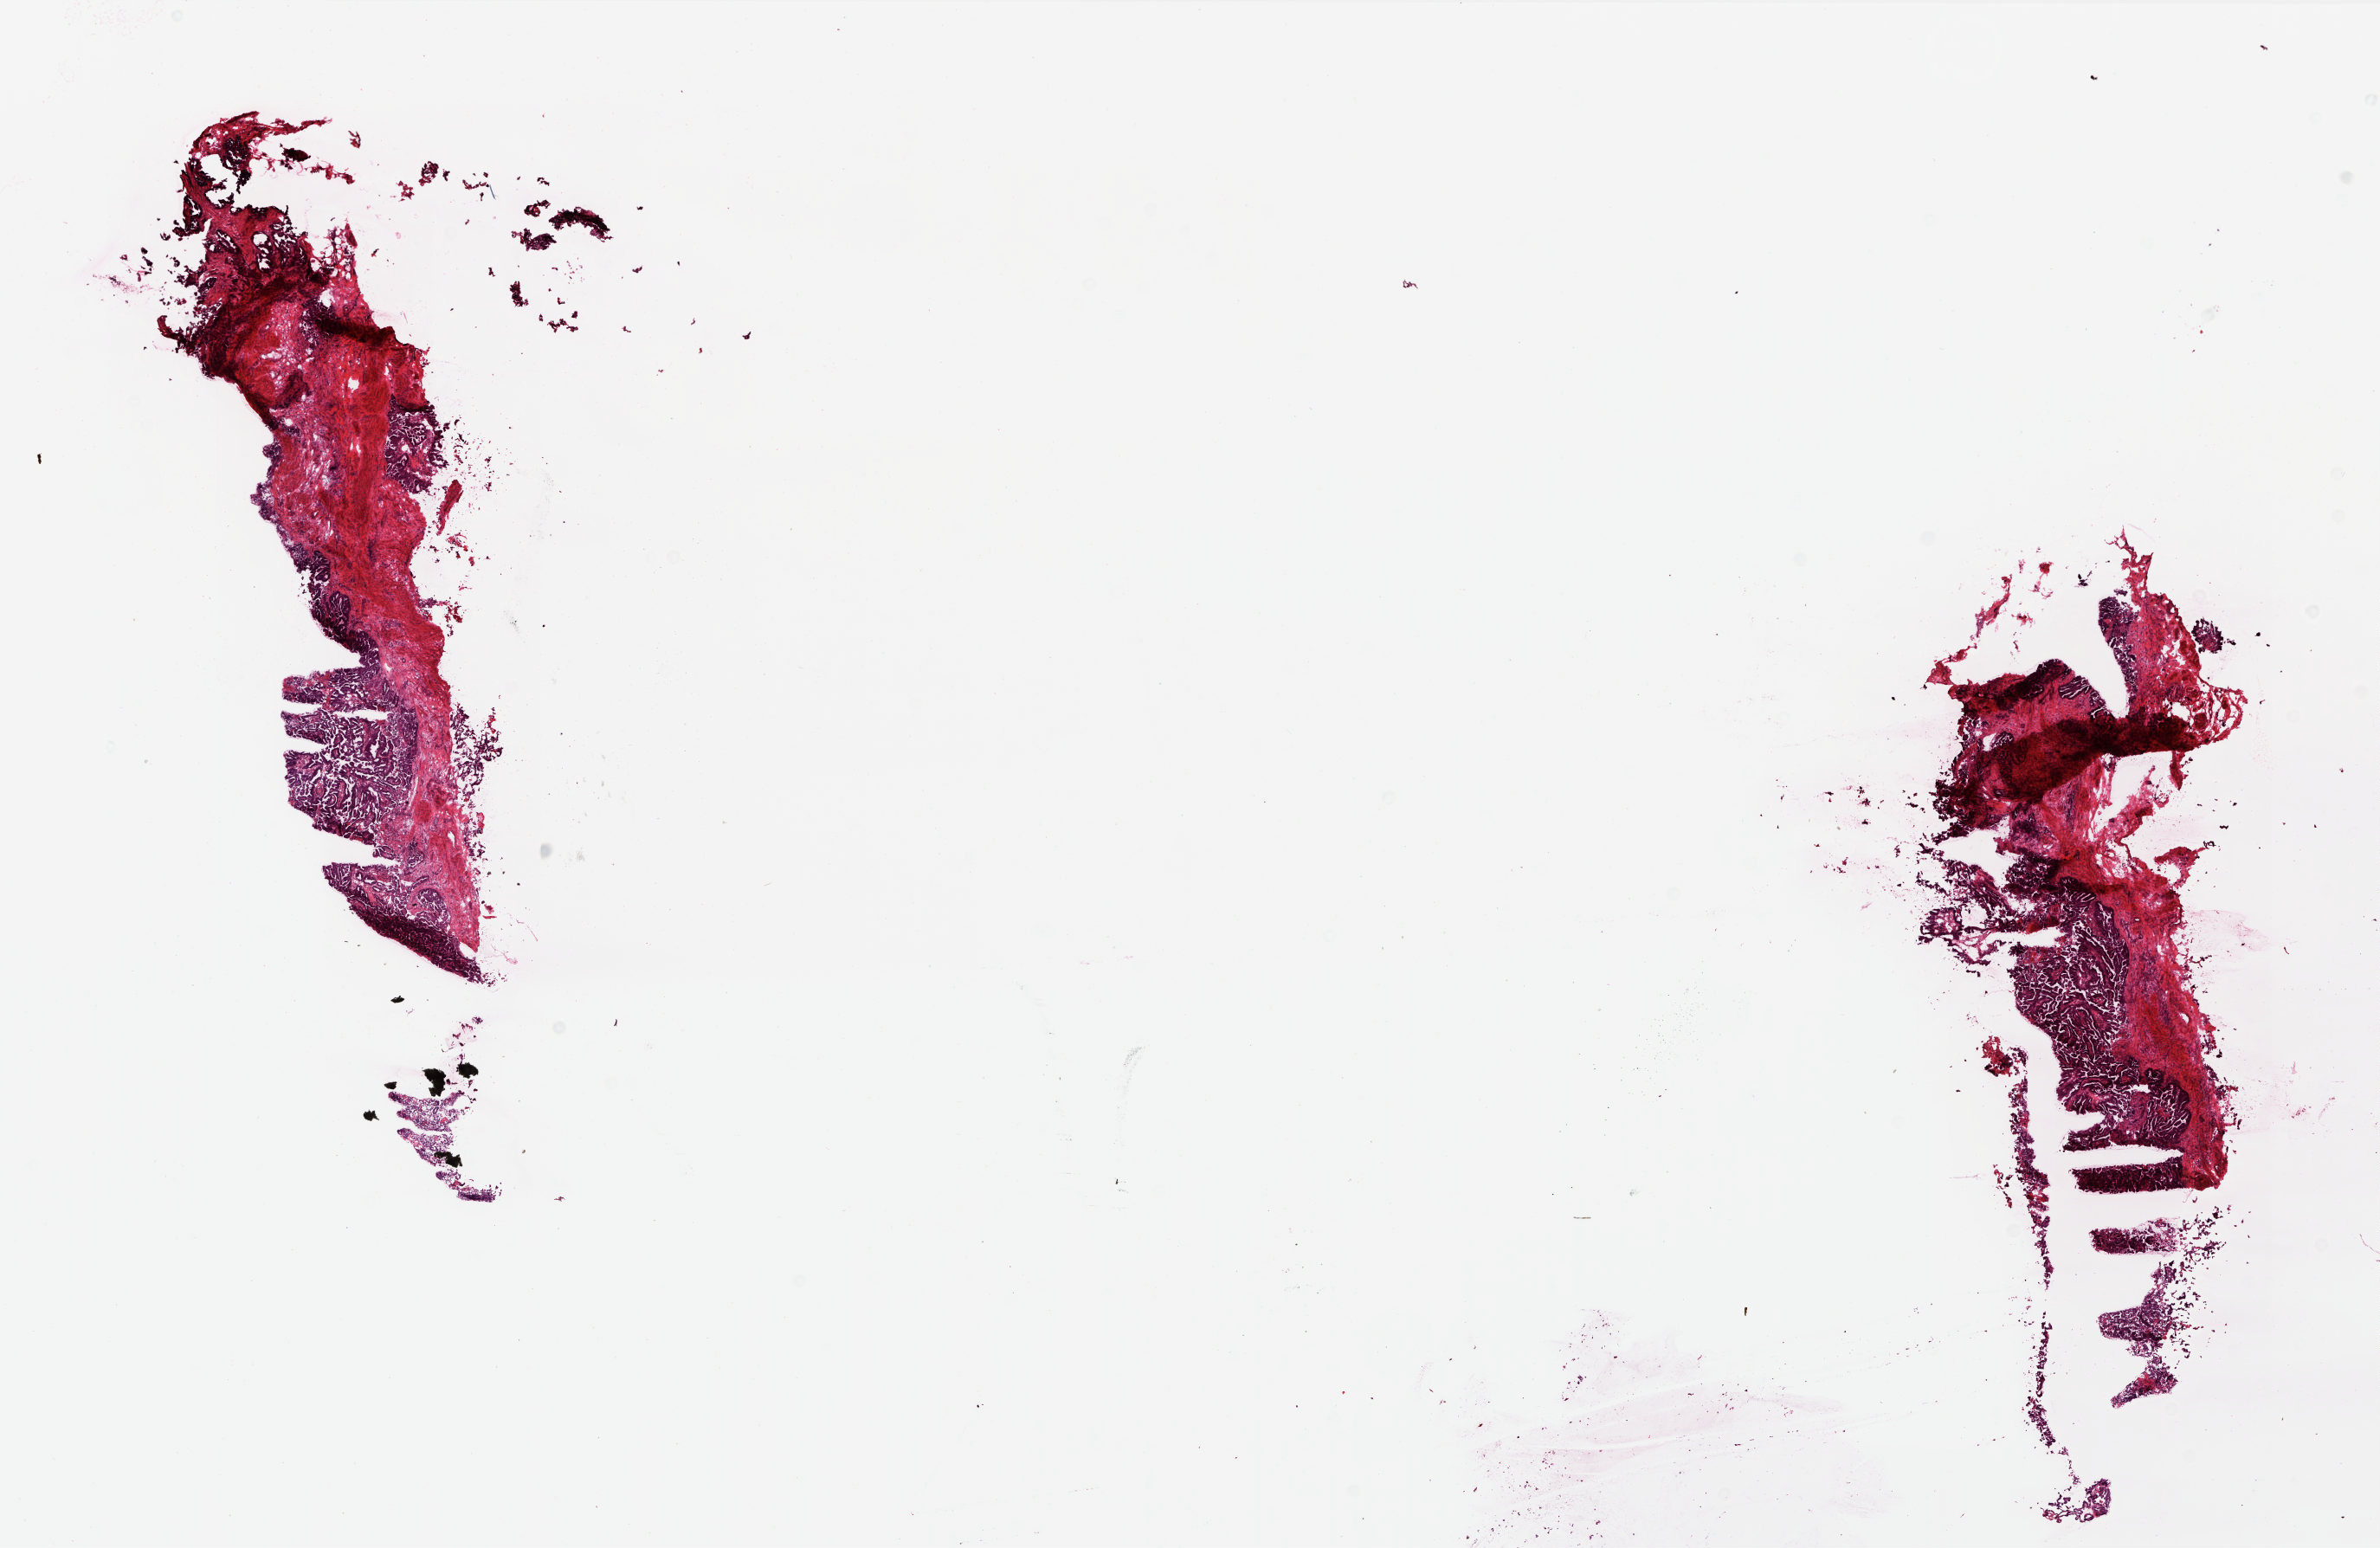
H&E-stained whole-slide image — shown as a low-resolution overview of the whole scanned area (about 22.0 x 14.3 mm), frozen section from the top of the tissue portion, sample: primary tumour, ovary. Female, age 80 years at initial diagnosis. Histologic grade: G2 (moderately differentiated). Pathologist review of this section (percent, as recorded): tumour cells 85%, tumour nuclei 95%, normal cells 0%, stromal cells 11%, necrosis 4%.
Laterality: bilateral. Diagnosis: Serous cystadenocarcinoma, NOS. FIGO stage: IV.